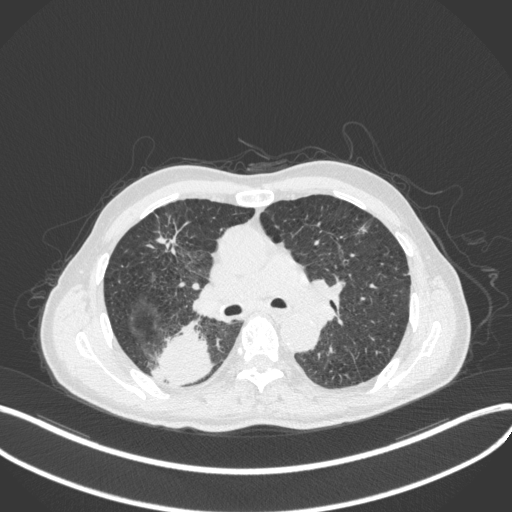
Chest CT, one axial slice. Position 278 of 423 along the scan axis. Reconstruction kernel B31f. 120 kVp. Lung window (W 1500 / L -600 HU). 512 × 512 image matrix, field of view 400 × 400 mm. Male patient, age 79 years. From the clinical record (not read from this slice): clinical TNM (as recorded): T3 N0 M0.
Structures marked on this image (bounding box drawn by a radiologist):
- lung tumour (recorded histology: adenocarcinoma): bounding box <152,314,214,385> (left, top, right, bottom; pixels)